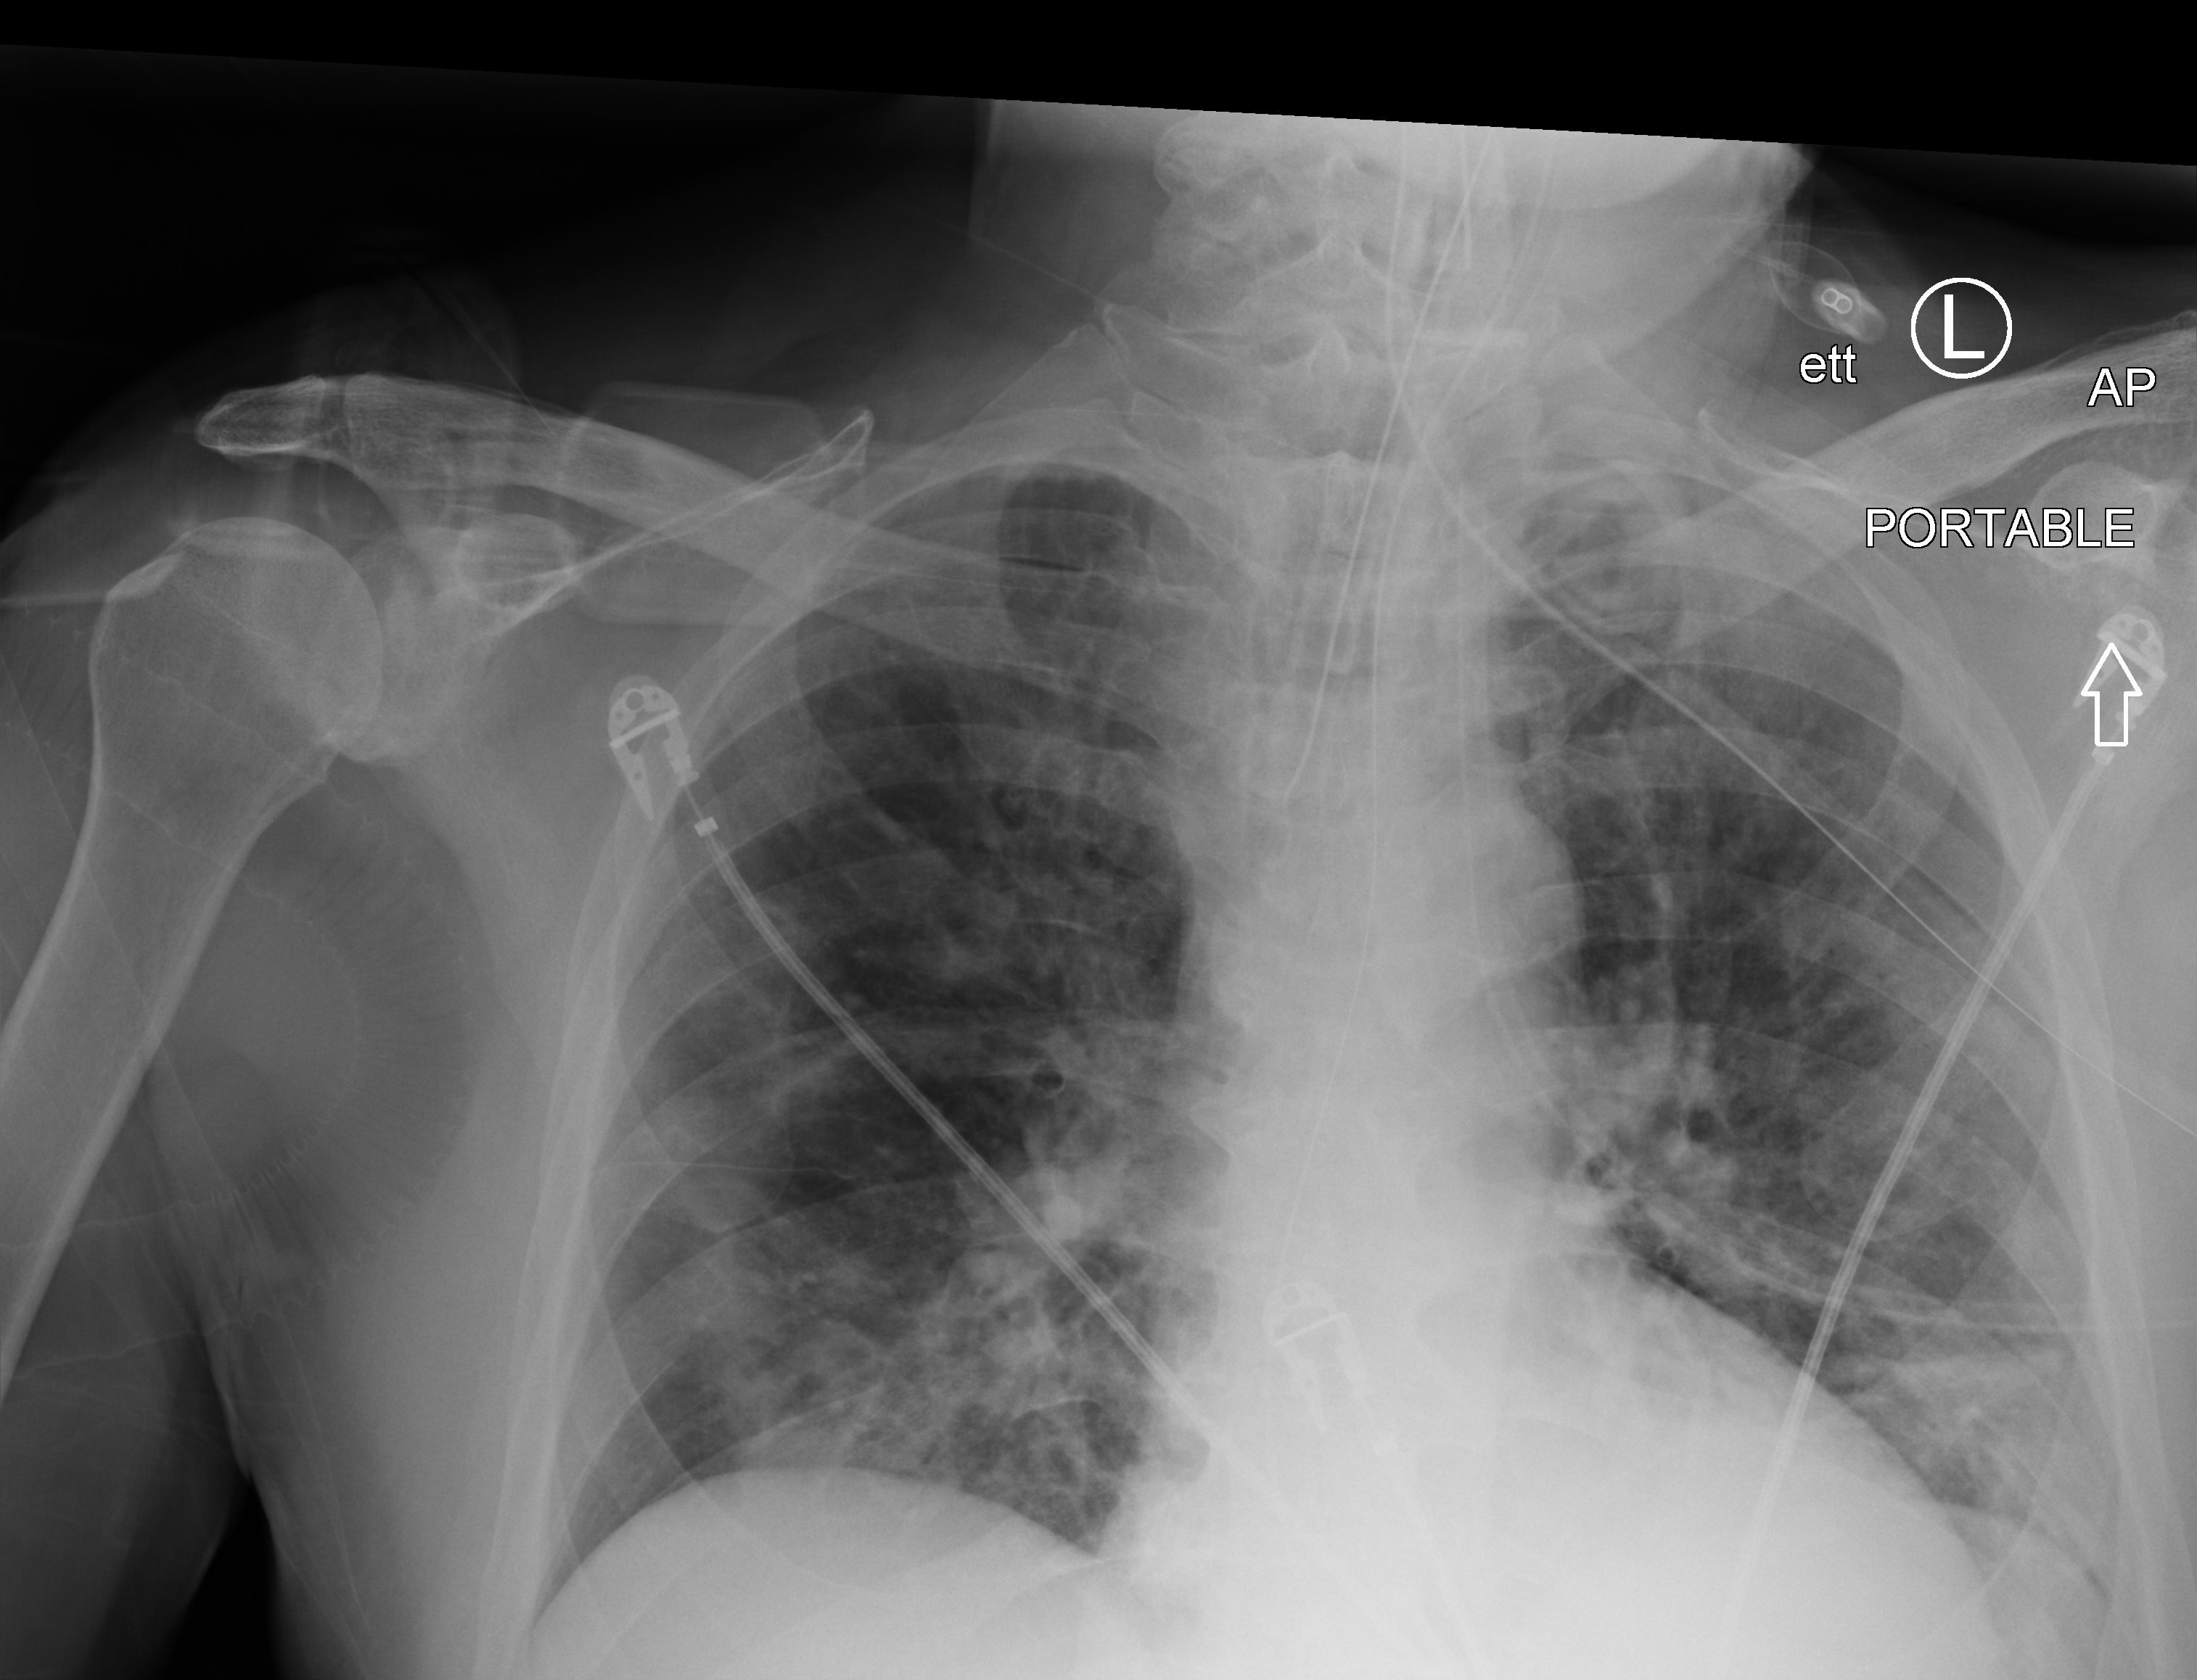
Bedside chest radiograph (computed radiography), anteroposterior (AP) projection. Patient hospitalised with COVID-19; male, aged 60–74 years.
Hospital-stay facts (about this admission, not read from this image; timing relative to this image not recorded):
- mechanically ventilated during this hospital stay: yes